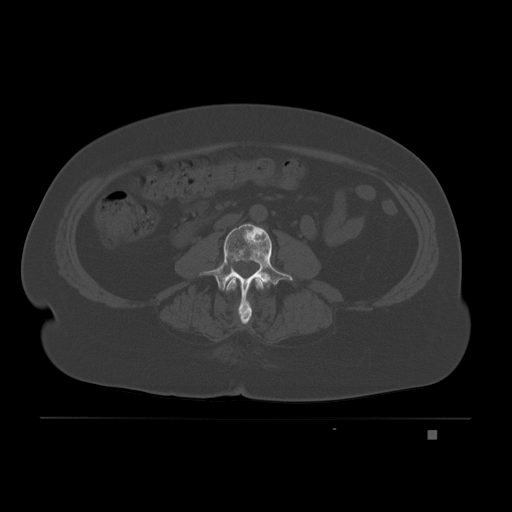
CT including the spine, one axial slice; position 52 of 221 along the scan axis; bone window (W 1800 / L 400 HU); 3 mm slice thickness; 512 × 512 image matrix, field of view 474 × 474 mm. Patient: female, 63 years. Case-level facts recorded for this patient, not image findings: primary cancer: breast.
Outlined on this slice (semi-automatic segmentation, software-assisted and operator-edited):
- L2 vertebra: bounding box [x1, y1, x2, y2] px = [225, 278, 264, 325]
- L3 vertebra: [199, 223, 293, 318]